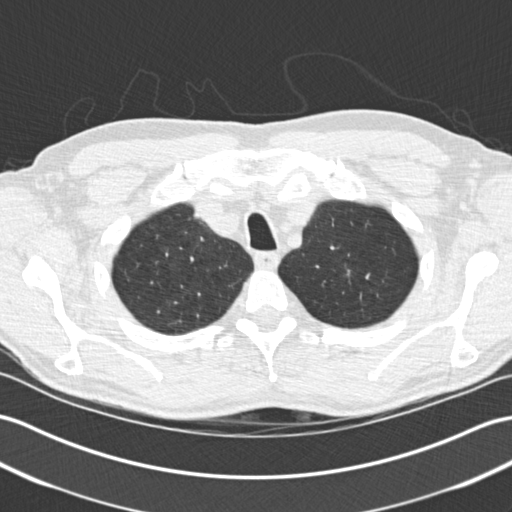
Axial slice from a low-dose chest CT screening exam. Baseline annual screen. Lung window (W 1500 / L -600 HU). Male participant, aged 64 years at enrolment. Former smoker at enrolment.
Lesion marked by an expert reader, bounding box (x1, y1, x2, y2) in pixels: (330, 259, 363, 290). Reader record for this screening exam (exam-level; its link to the box is not recorded): non-calcified nodule or mass ≥4 mm, right upper lobe, 7 × 5 mm, spiculated (stellate) margins, soft tissue attenuation. Note: the box lies in the patient's left hemithorax on this image, whereas the reader's record names the right lung; they may be different findings. Official screen result: positive, change unspecified: nodule(s) >= 4 mm or enlarging nodule(s), mass(es), or other non-specific abnormalities suspicious for lung cancer. Later outcome: lung cancer diagnosed 833 days after this screen (after the third annual screen) — adenocarcinoma, NOS, left upper lobe, poorly differentiated (G3), stage IA (AJCC 6th edition), 10 mm at pathology.